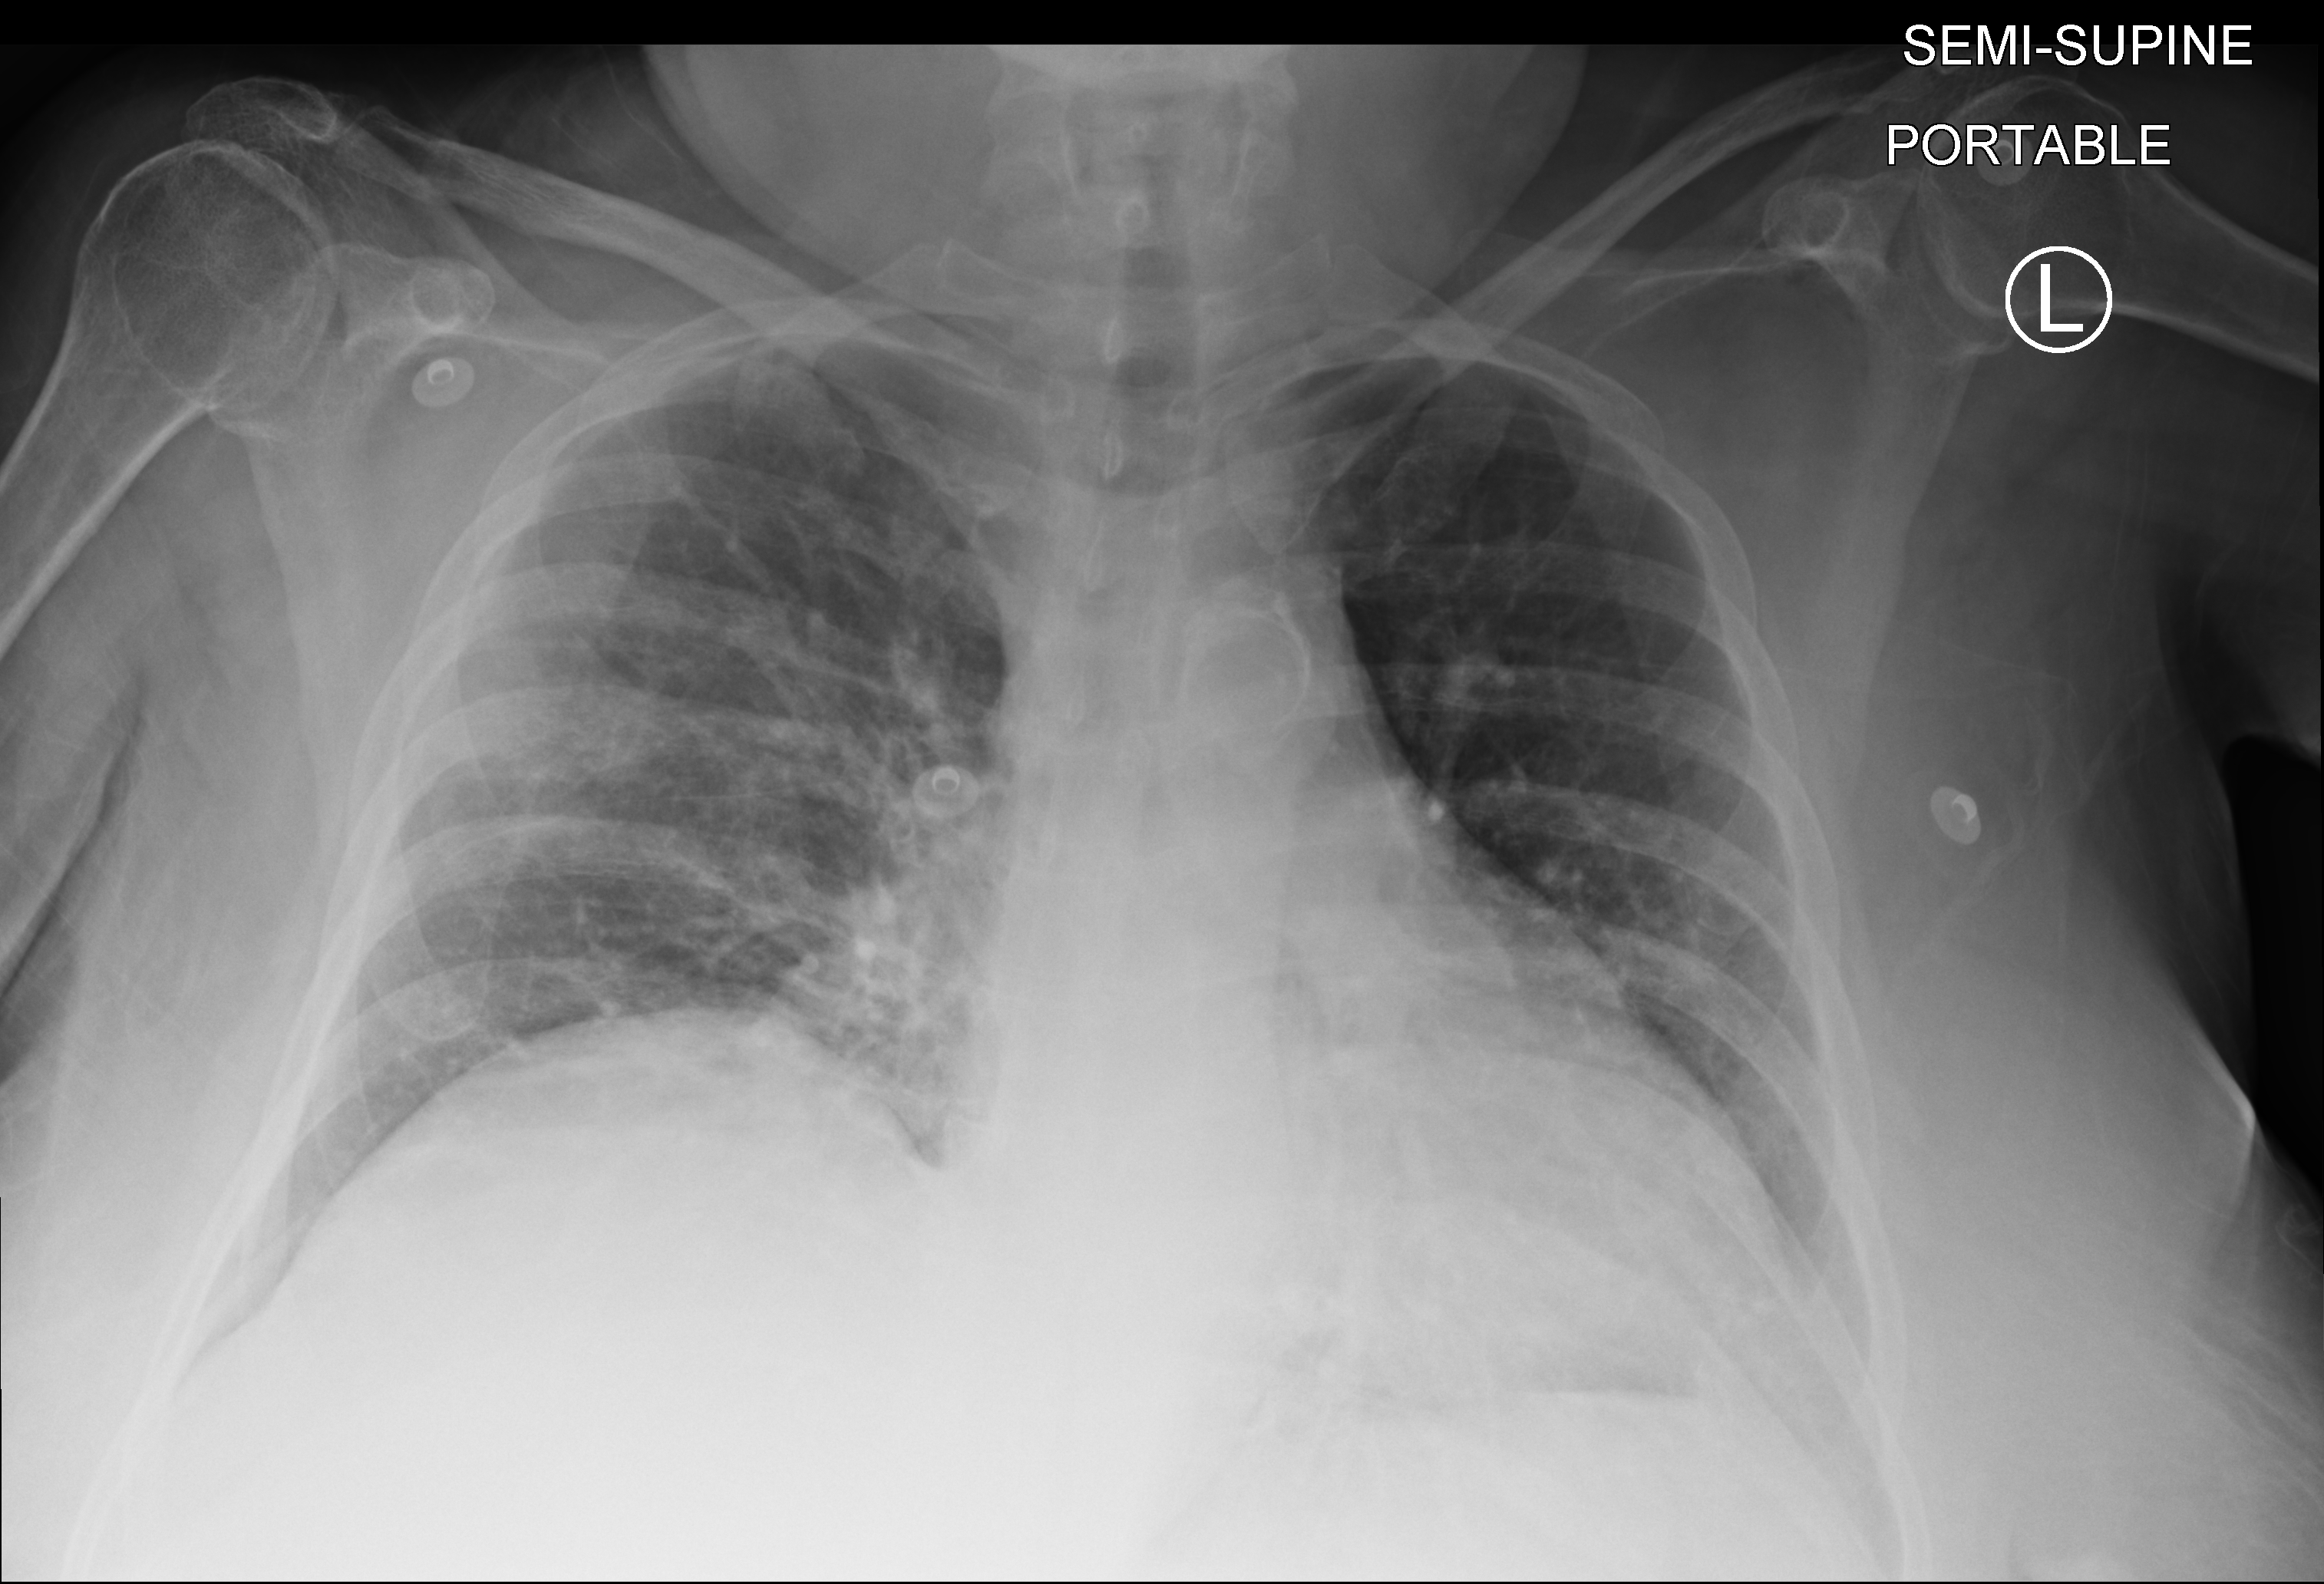
Portable chest radiograph; anteroposterior (AP) projection. Patient hospitalised with COVID-19; female, aged 60–74 years.
From the hospital-stay record, not from the radiograph (when in the stay this image was taken is not recorded): length of hospital stay: 8 days.